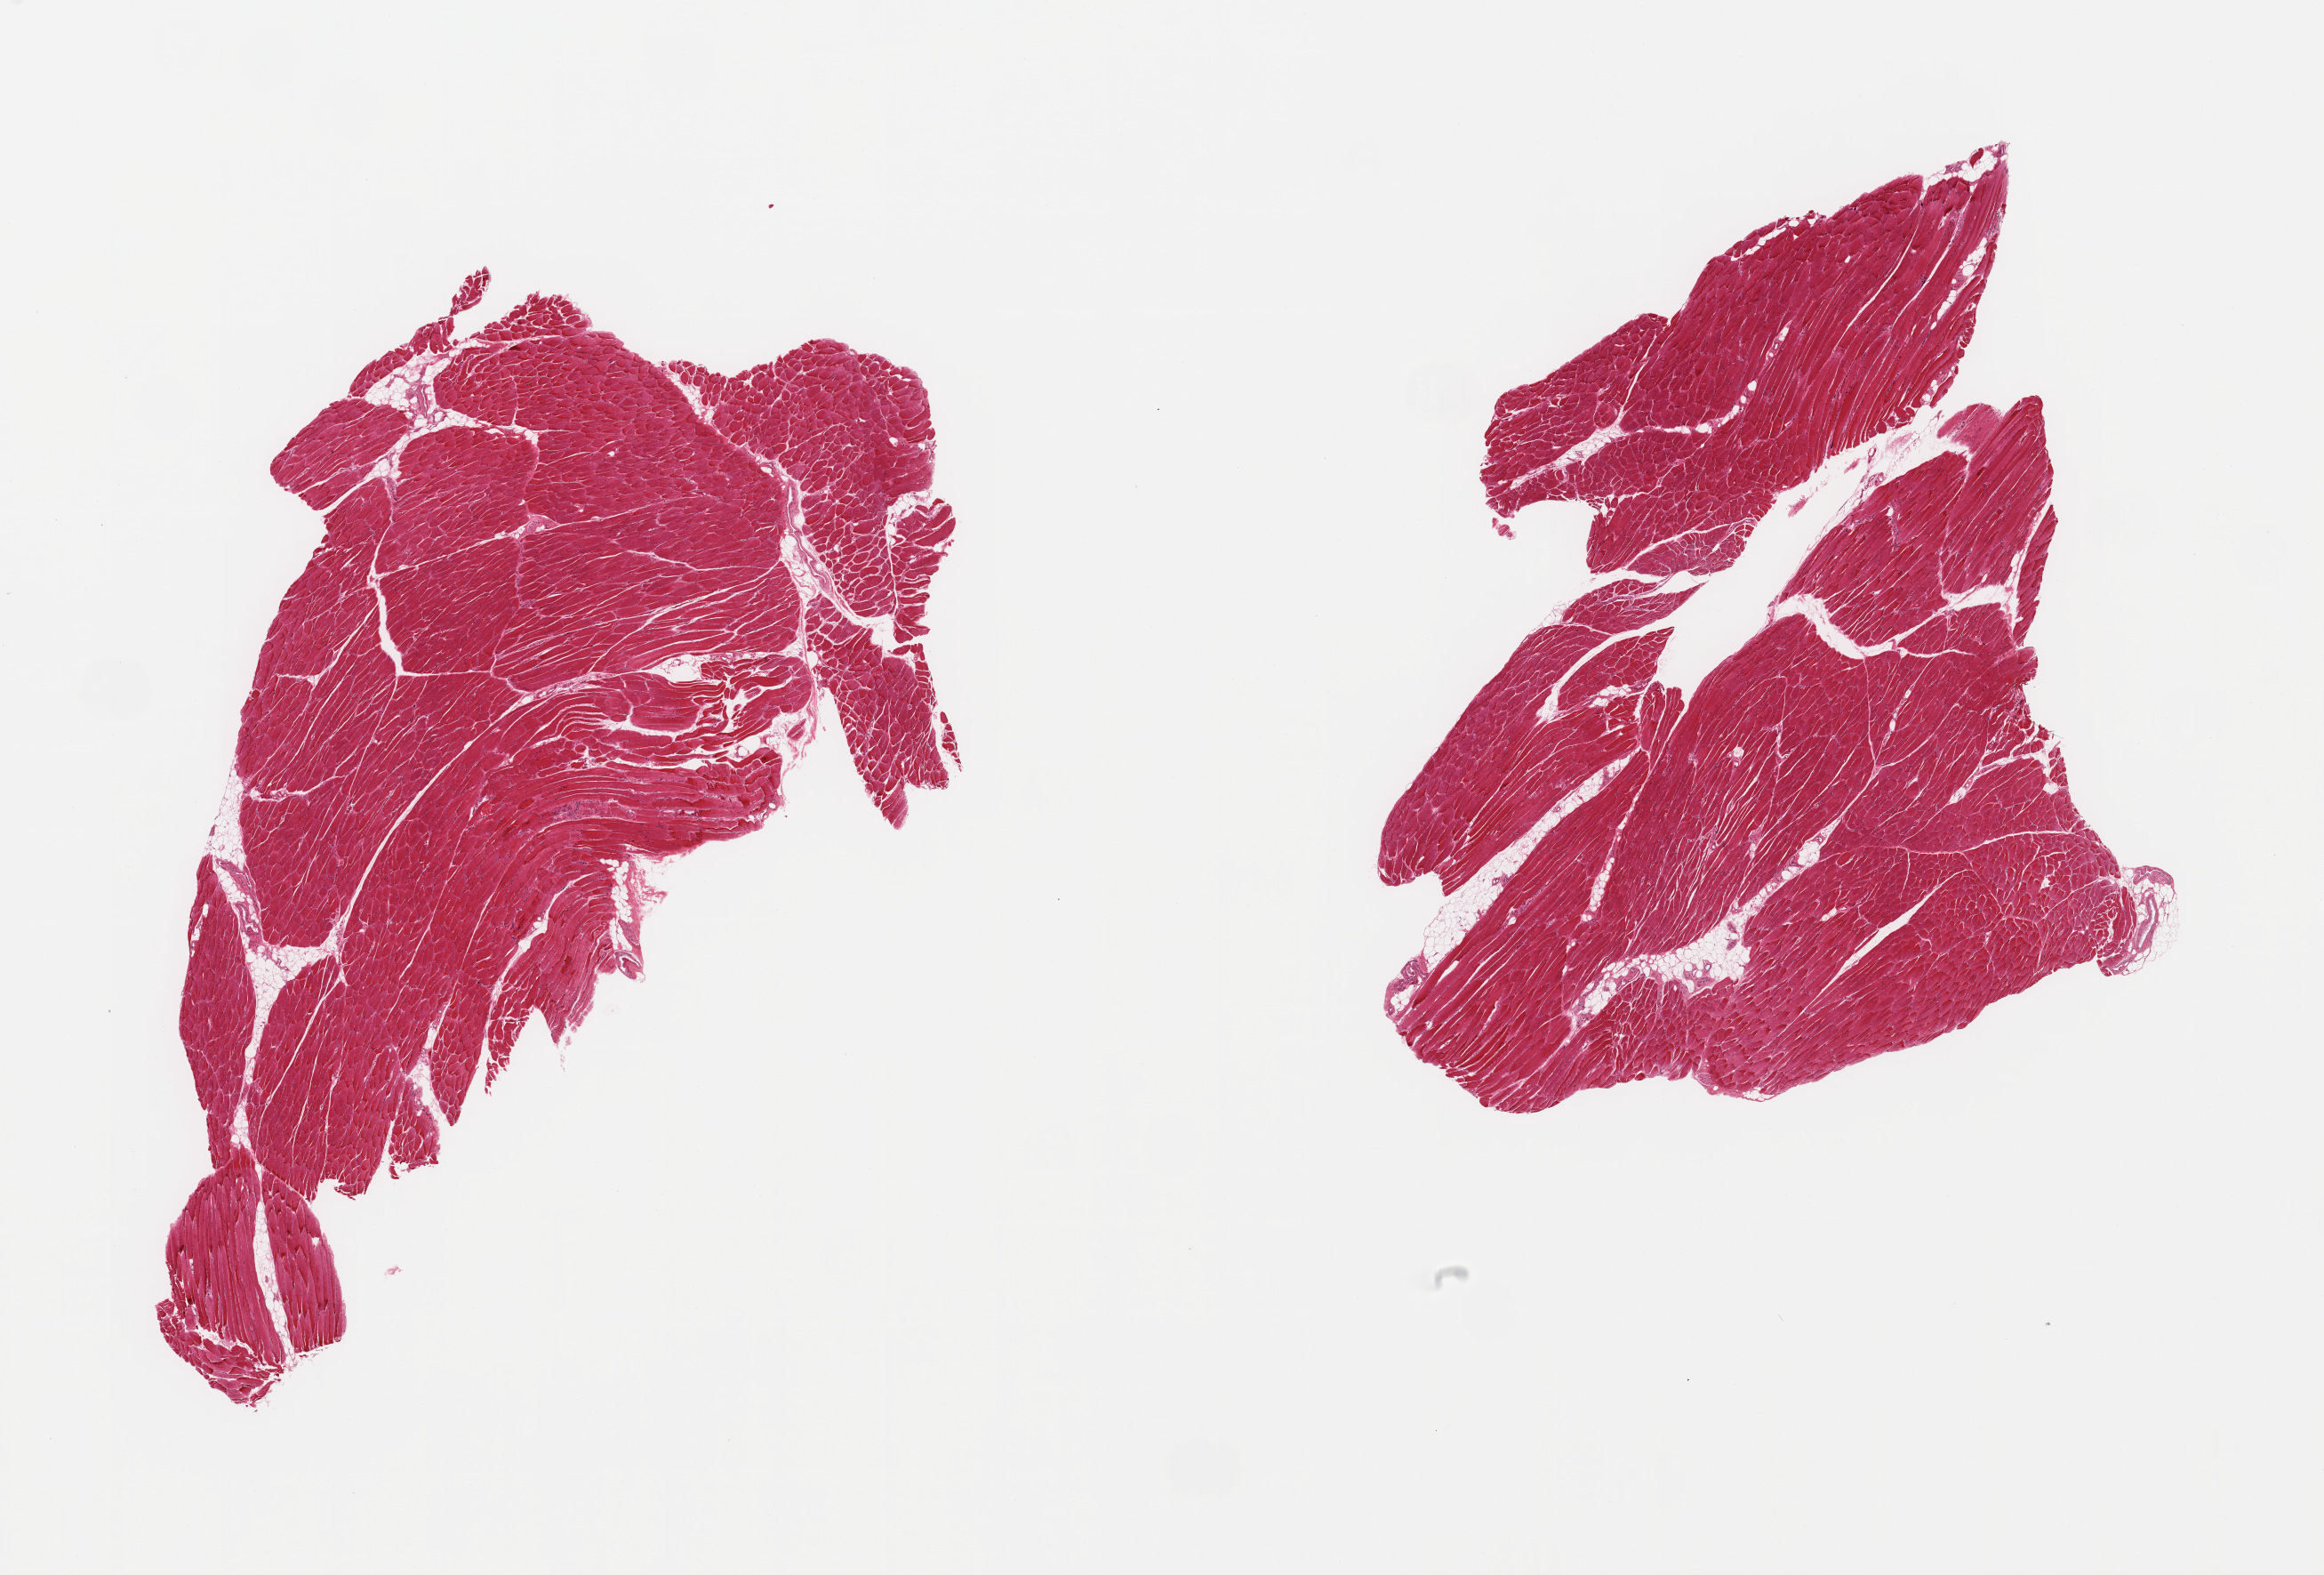
Hematoxylin and eosin (H&E) whole-slide image, brightfield, low-resolution overview of the scanned area, about 20.7 x 14.0 mm, PAXgene-fixed, paraffin-embedded tissue, section of skeletal muscle (target tissue), donor tissue sample. Male donor.
Reviewer comment on this tissue sample: 2 pieces; interstitial fat/vascular elemements are ~10% tissue.